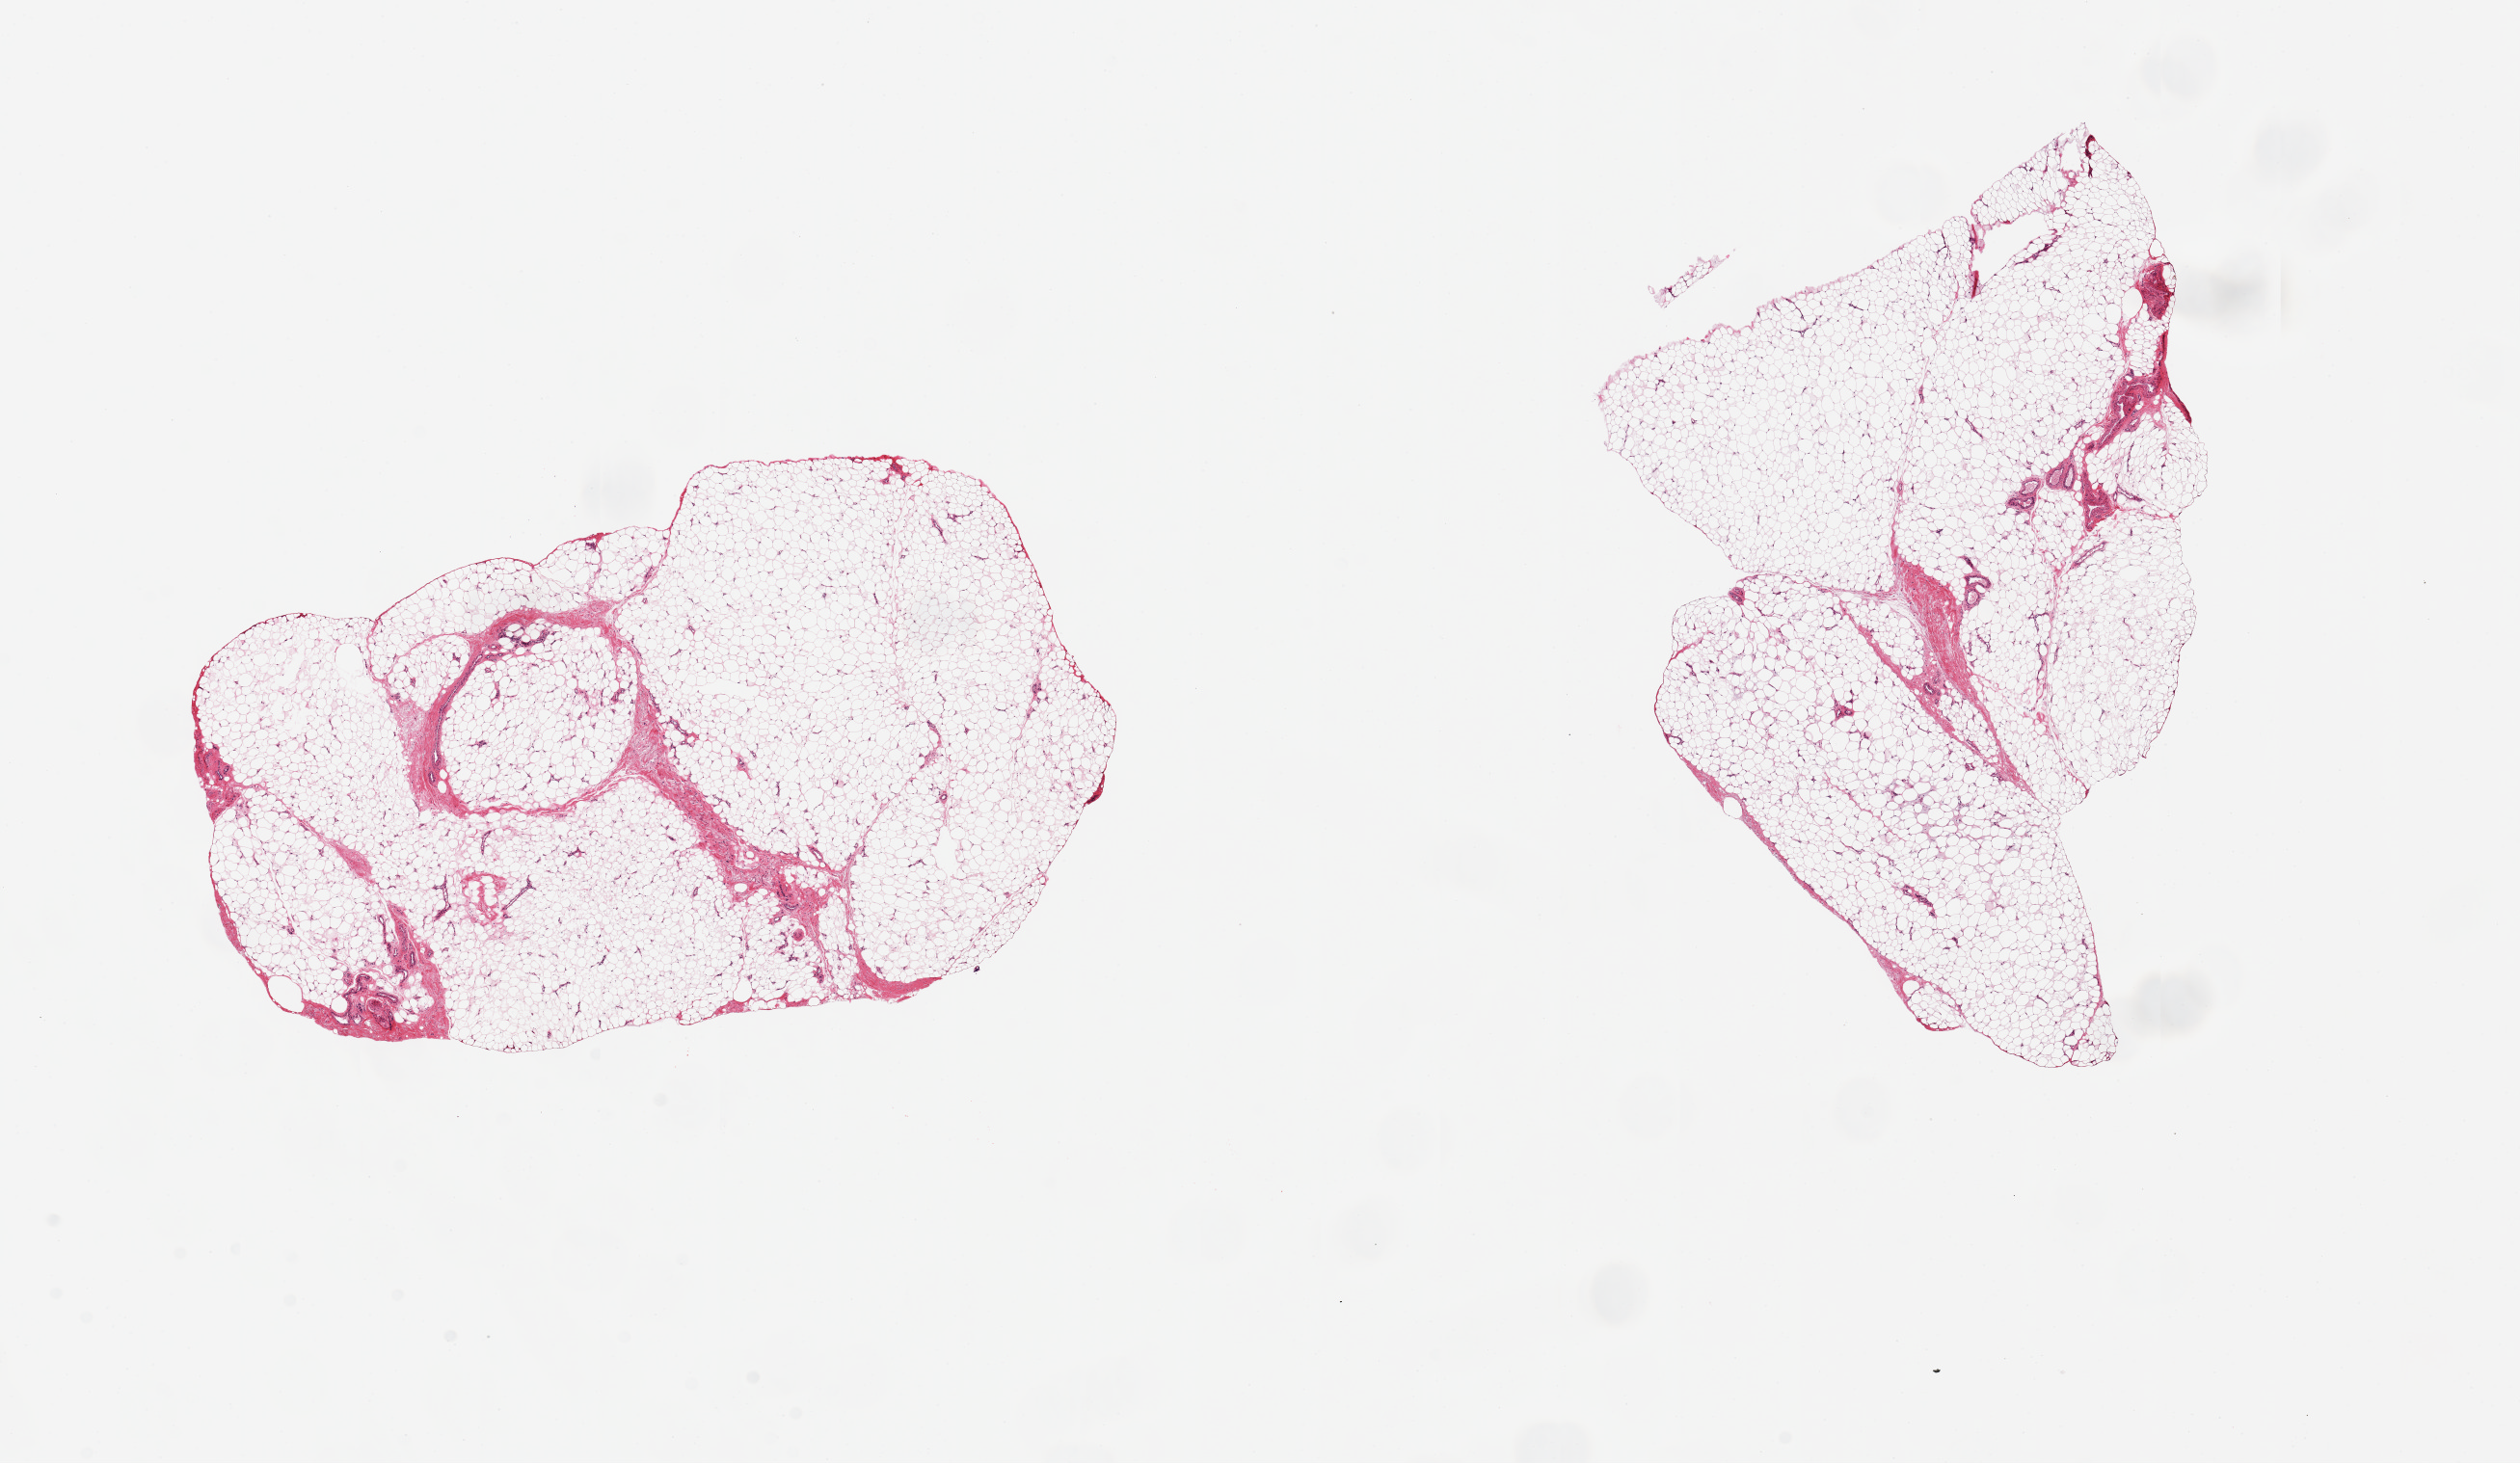
Whole-slide image, haematoxylin and eosin stain — shown as a low-resolution overview of the whole scanned area (about 20.7 x 12.0 mm). PAXgene-fixed, paraffin-embedded tissue. Sampled site (target tissue): adipose tissue. Donor tissue sample.
Review note (as recorded): 2 pieces, 8x5 & 8x5mm; no artifacts.